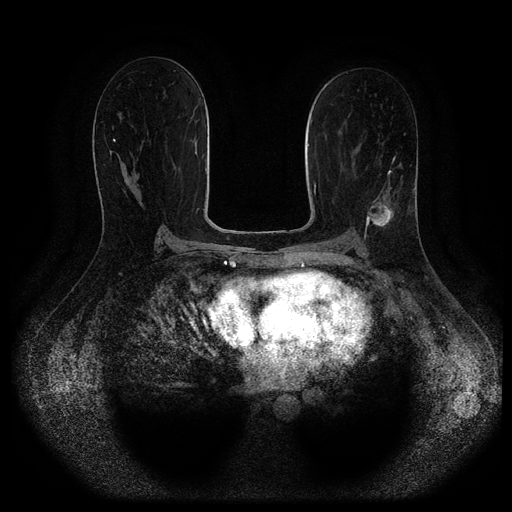
Breast MRI (dynamic contrast-enhanced, multi-phase), one axial slice; slice 58 of 116 in the series (ordered by position); dynamic contrast-enhanced series, time point 2 of 5 at this slice position (early post-contrast); 1.5 T; TE 2.6 ms, TR 5.3 ms; 2 mm slice thickness; 512 × 512 image matrix. Female patient, age 45 years.
Outlined on this slice (semi-automatic segmentation, software-assisted and operator-edited):
- breast lesion (labelled 'tumour' in the annotation; benign lesions carry a separate 'benign' label): bounding box (x1, y1, x2, y2) in pixels: (367, 197, 394, 228)